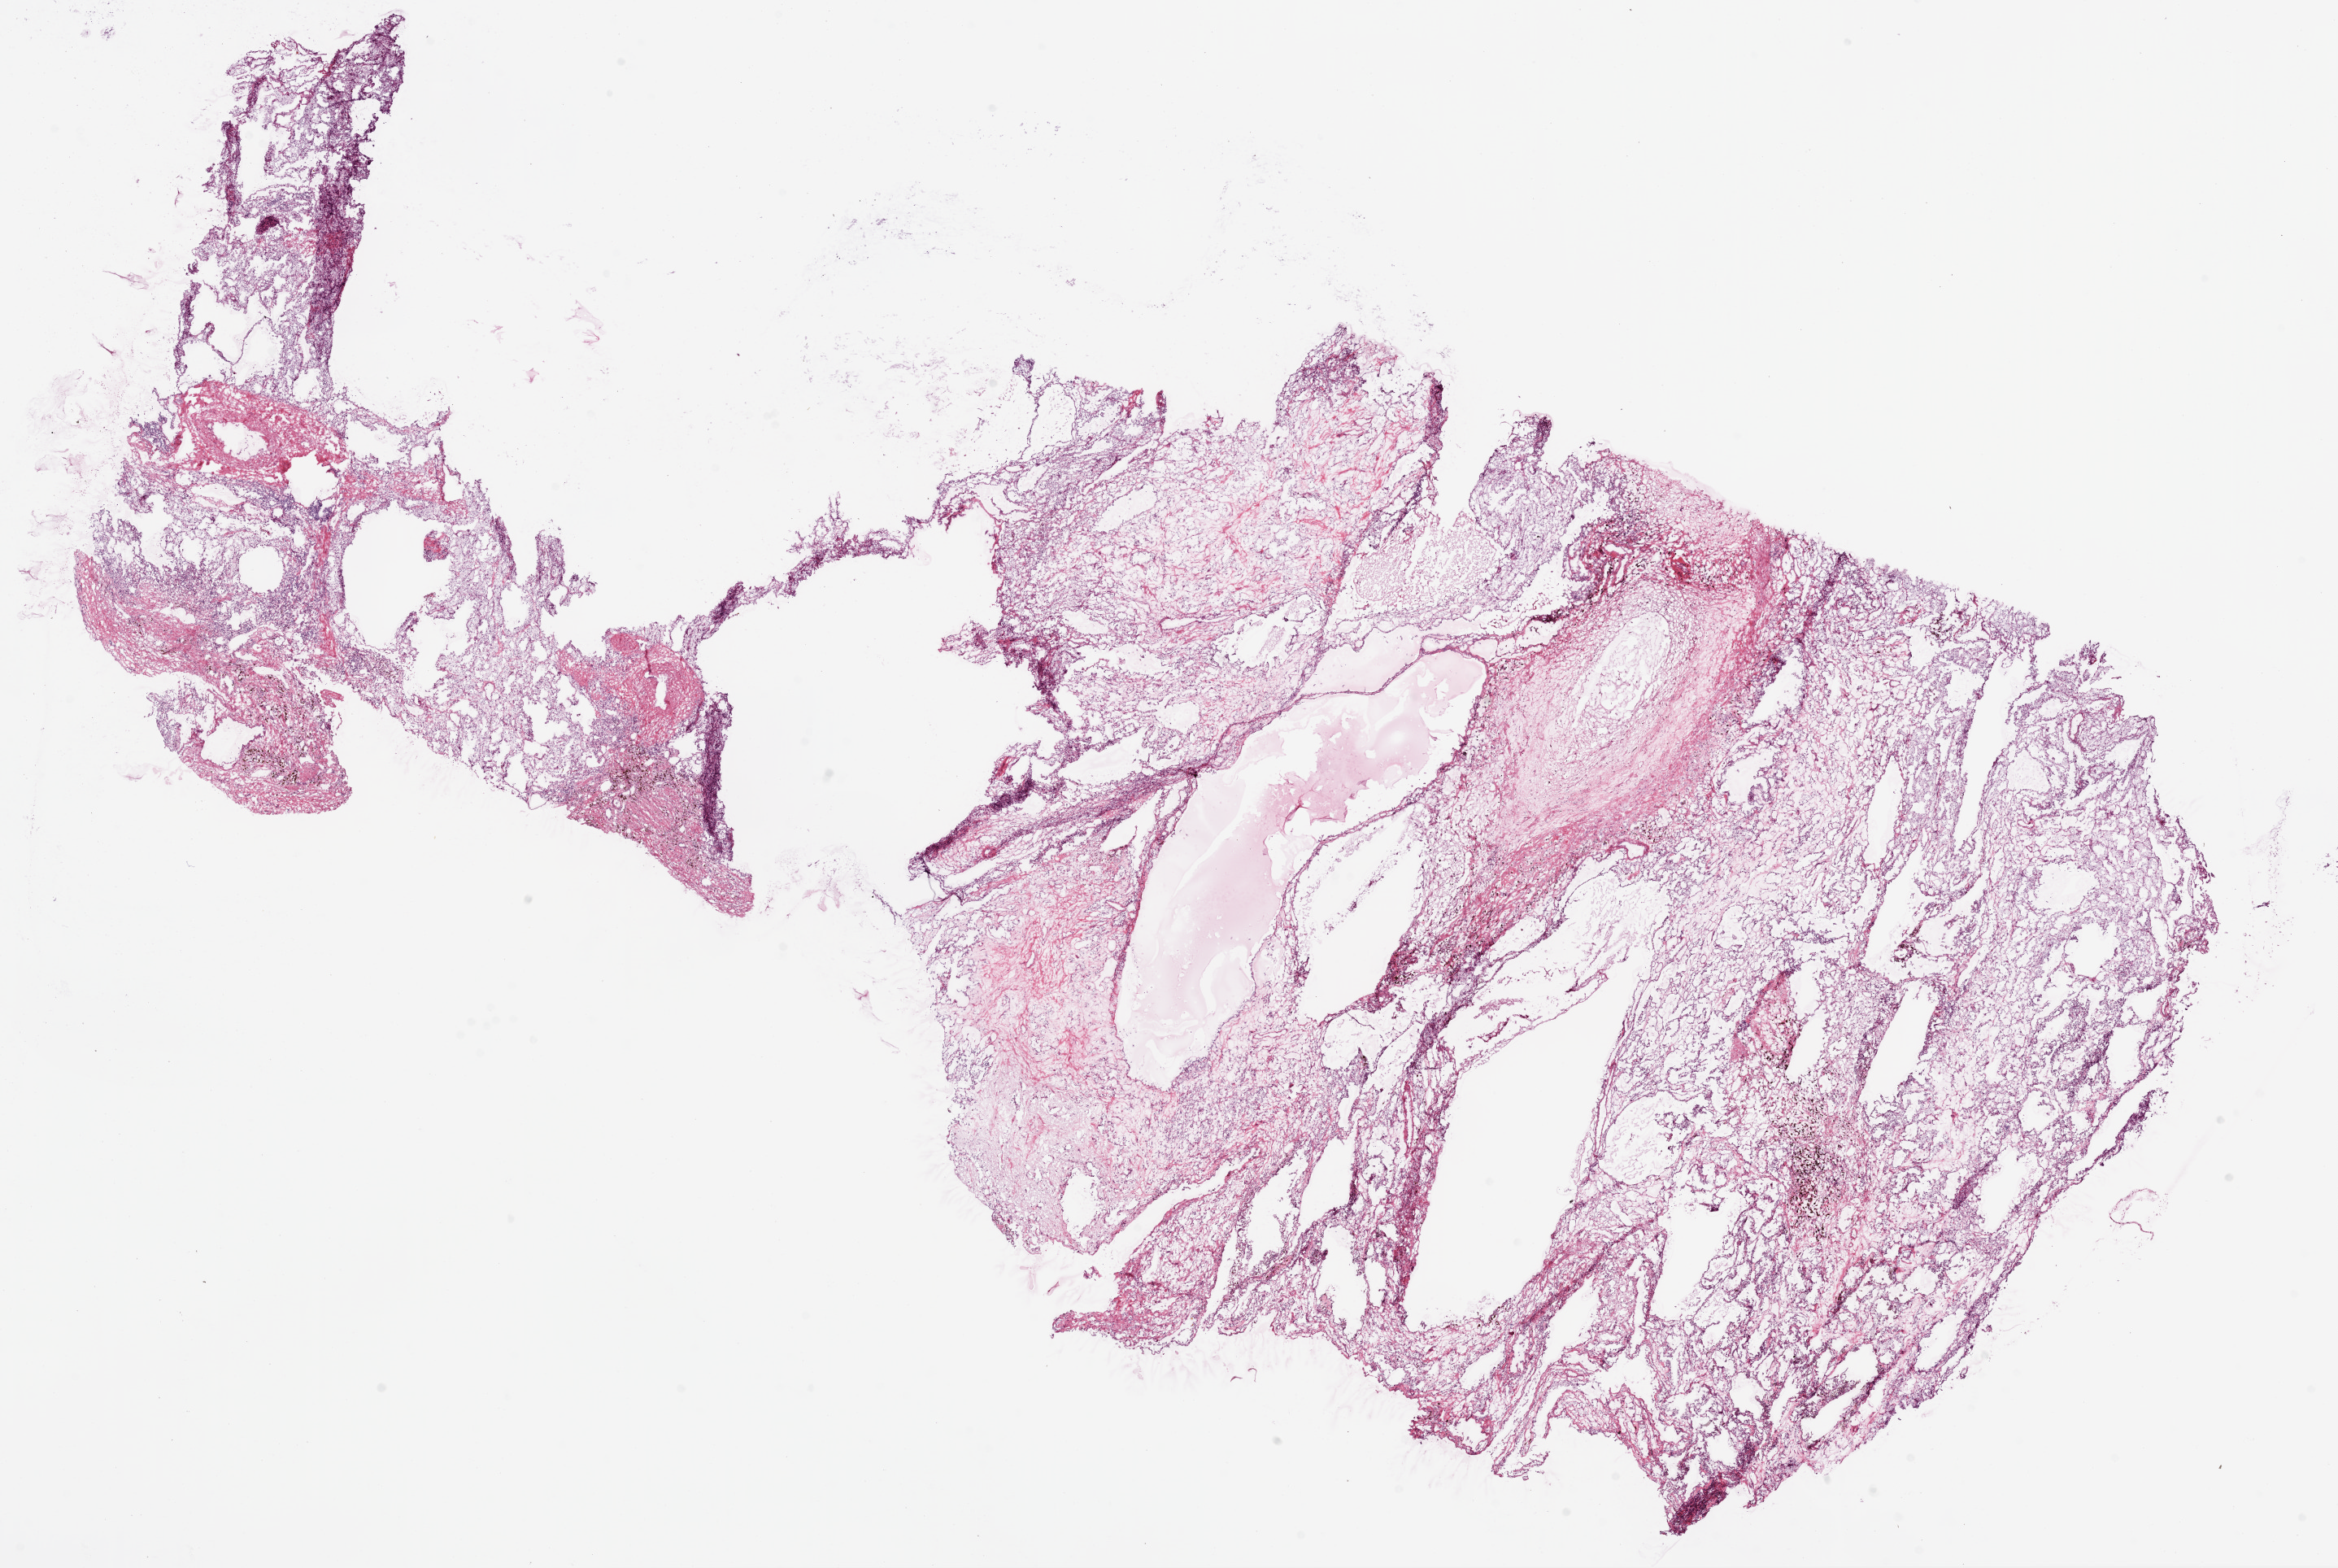
Hematoxylin and eosin (H&E) stained whole-slide image, whole scanned area (about 23.1 x 15.5 mm, slide scanned at 20x) shown as a low-resolution overview, frozen section, kidney, primary tumour sample. Male patient; age at initial diagnosis 88 years. Histologic grade: G2 (moderately differentiated). Composition of this section per pathologist review: tumour cells 85%, tumour nuclei 85%, normal cells 0%, stromal cells 15%, necrosis 0%.
TNM: T1a N0 M0. AJCC pathologic stage: I. Histologic diagnosis: Clear cell adenocarcinoma, NOS.